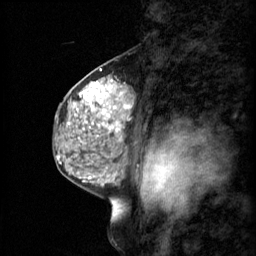
Breast MRI (dynamic contrast-enhanced), one sagittal slice; position 37 of 60 along the scan axis; 3 images stored at this slice position (order not interpretable as contrast timing); 1.5 T; TE 4.2 ms, TR 11 ms; 2 mm slice thickness; 256 × 256 image matrix, field of view 200 × 200 mm. Patient: female, 48 years.
Structures marked on this image (semi-automatically segmented with operator editing):
- analysis volume of interest (the breast-tissue region the enhancement analysis was run in; not a lesion): bounding box (x1, y1, x2, y2) in pixels: (69, 74, 132, 147)
- tumour enhancement mask (voxels above the 70 % enhancement threshold inside the analysis volume of interest): (69, 80, 130, 143)